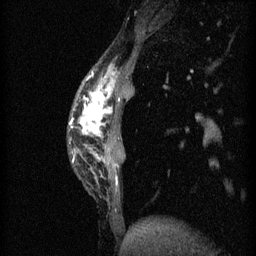
Breast MRI (dynamic contrast-enhanced), one sagittal slice. Slice 12 of 60 in the series (ordered by position). 3 images stored at this slice position (order not interpretable as contrast timing). 1.5 T. TE 4.2 ms, TR 11 ms. 2 mm slice thickness. 256 × 256 image matrix, field of view 180 × 180 mm. Patient: female, 40 years.
Structures marked on this image (semi-automatic segmentation, software-assisted and operator-edited):
- analysis volume of interest (the breast-tissue region the enhancement analysis was run in; not a lesion): bounding box [x1, y1, x2, y2] px = [70, 66, 135, 191]
- tumour enhancement mask (voxels above the 70 % enhancement threshold inside the analysis volume of interest): [70, 76, 119, 183]